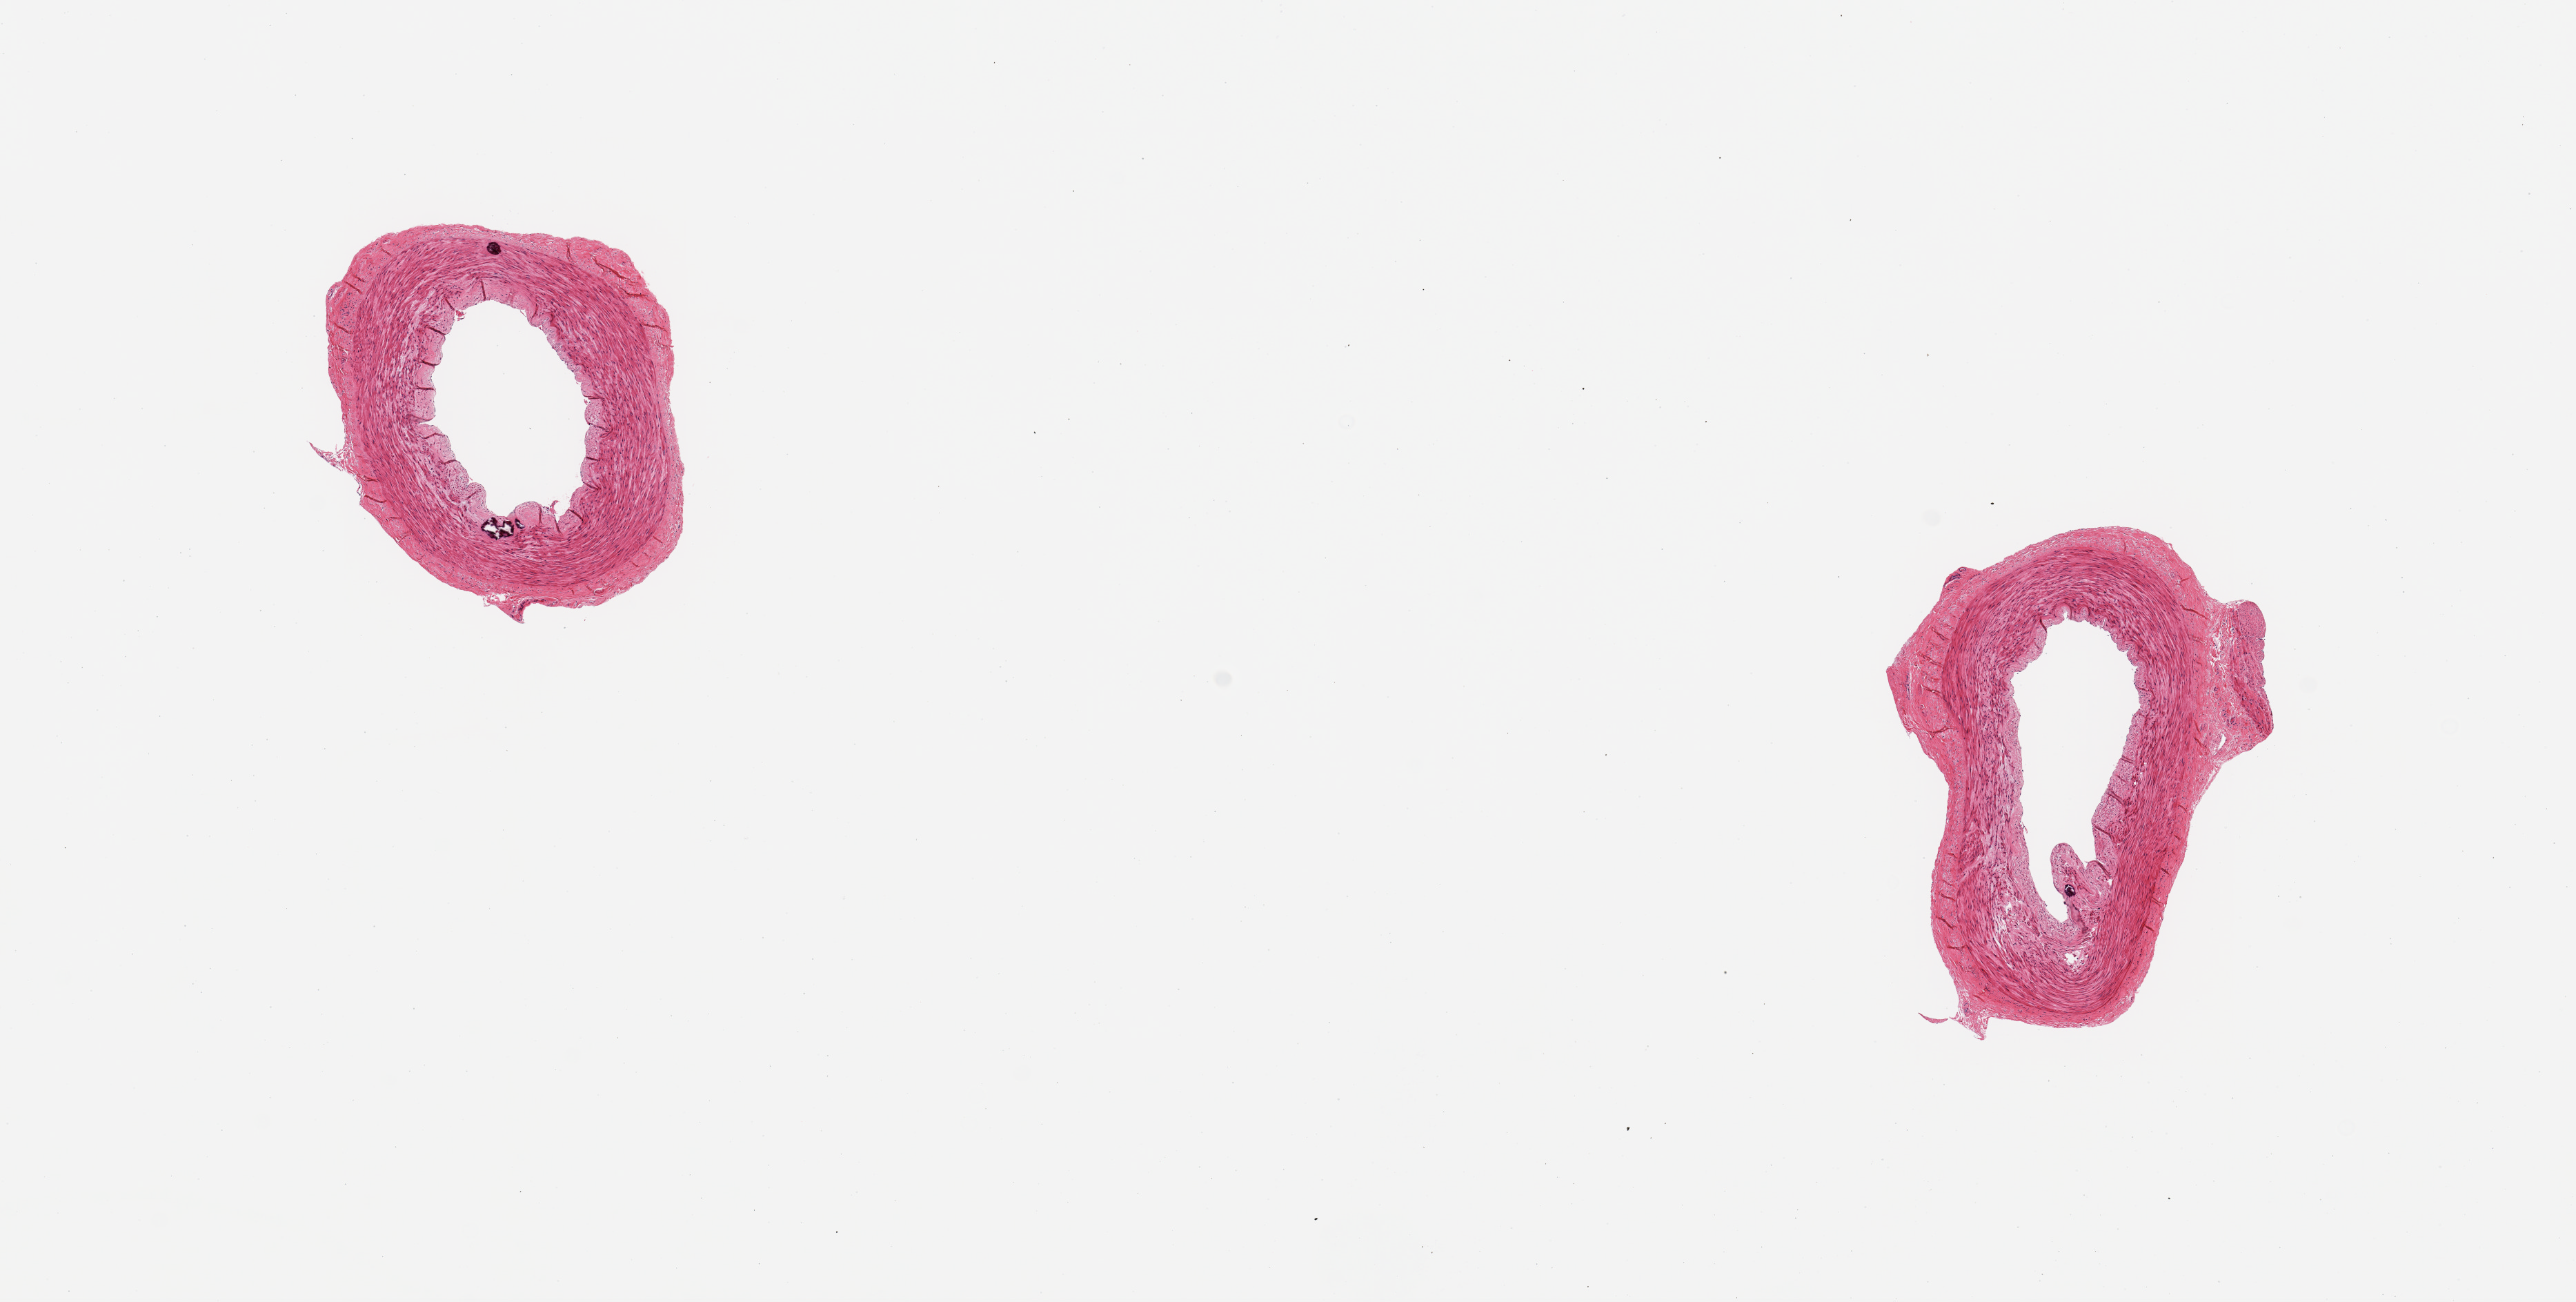
Hematoxylin and eosin (H&E) whole-slide image, whole scanned area (about 14.8 x 7.5 mm) shown as a low-resolution overview. PAXgene-fixed paraffin-embedded (PFPE) section. Section of tibial artery (target tissue). Donor tissue sample. Male donor.
Pathologist's review note for this sample: 2 pieces; several small (0.2 mm) focal calcifications but no plaques.